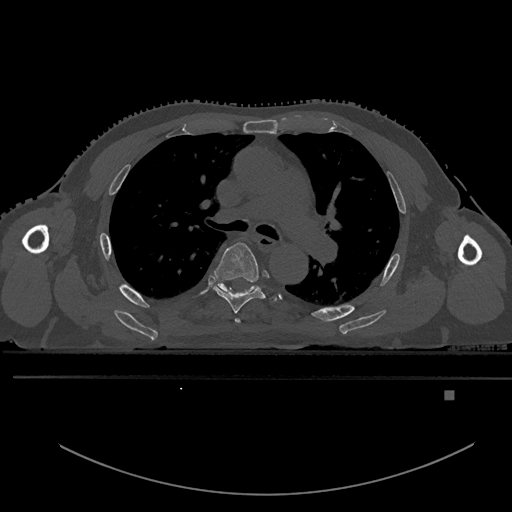
CT including the spine, one axial slice; slice 353 of 969 in the series (ordered by position); bone window (W 1800 / L 400 HU); 0.5 mm slice thickness; 512 × 512 image matrix, field of view 456 × 456 mm. Patient: male, 82 years. Case-level facts recorded for this patient, not image findings: primary cancer: prostate.
Outlined on this slice (semi-automatic segmentation, software-assisted and operator-edited):
- T4 vertebra: box from (x=235, y=318) to (x=240, y=324) px
- T5 vertebra: (x=213, y=242)–(x=277, y=313)
- T6 vertebra: (x=212, y=284)–(x=255, y=293)